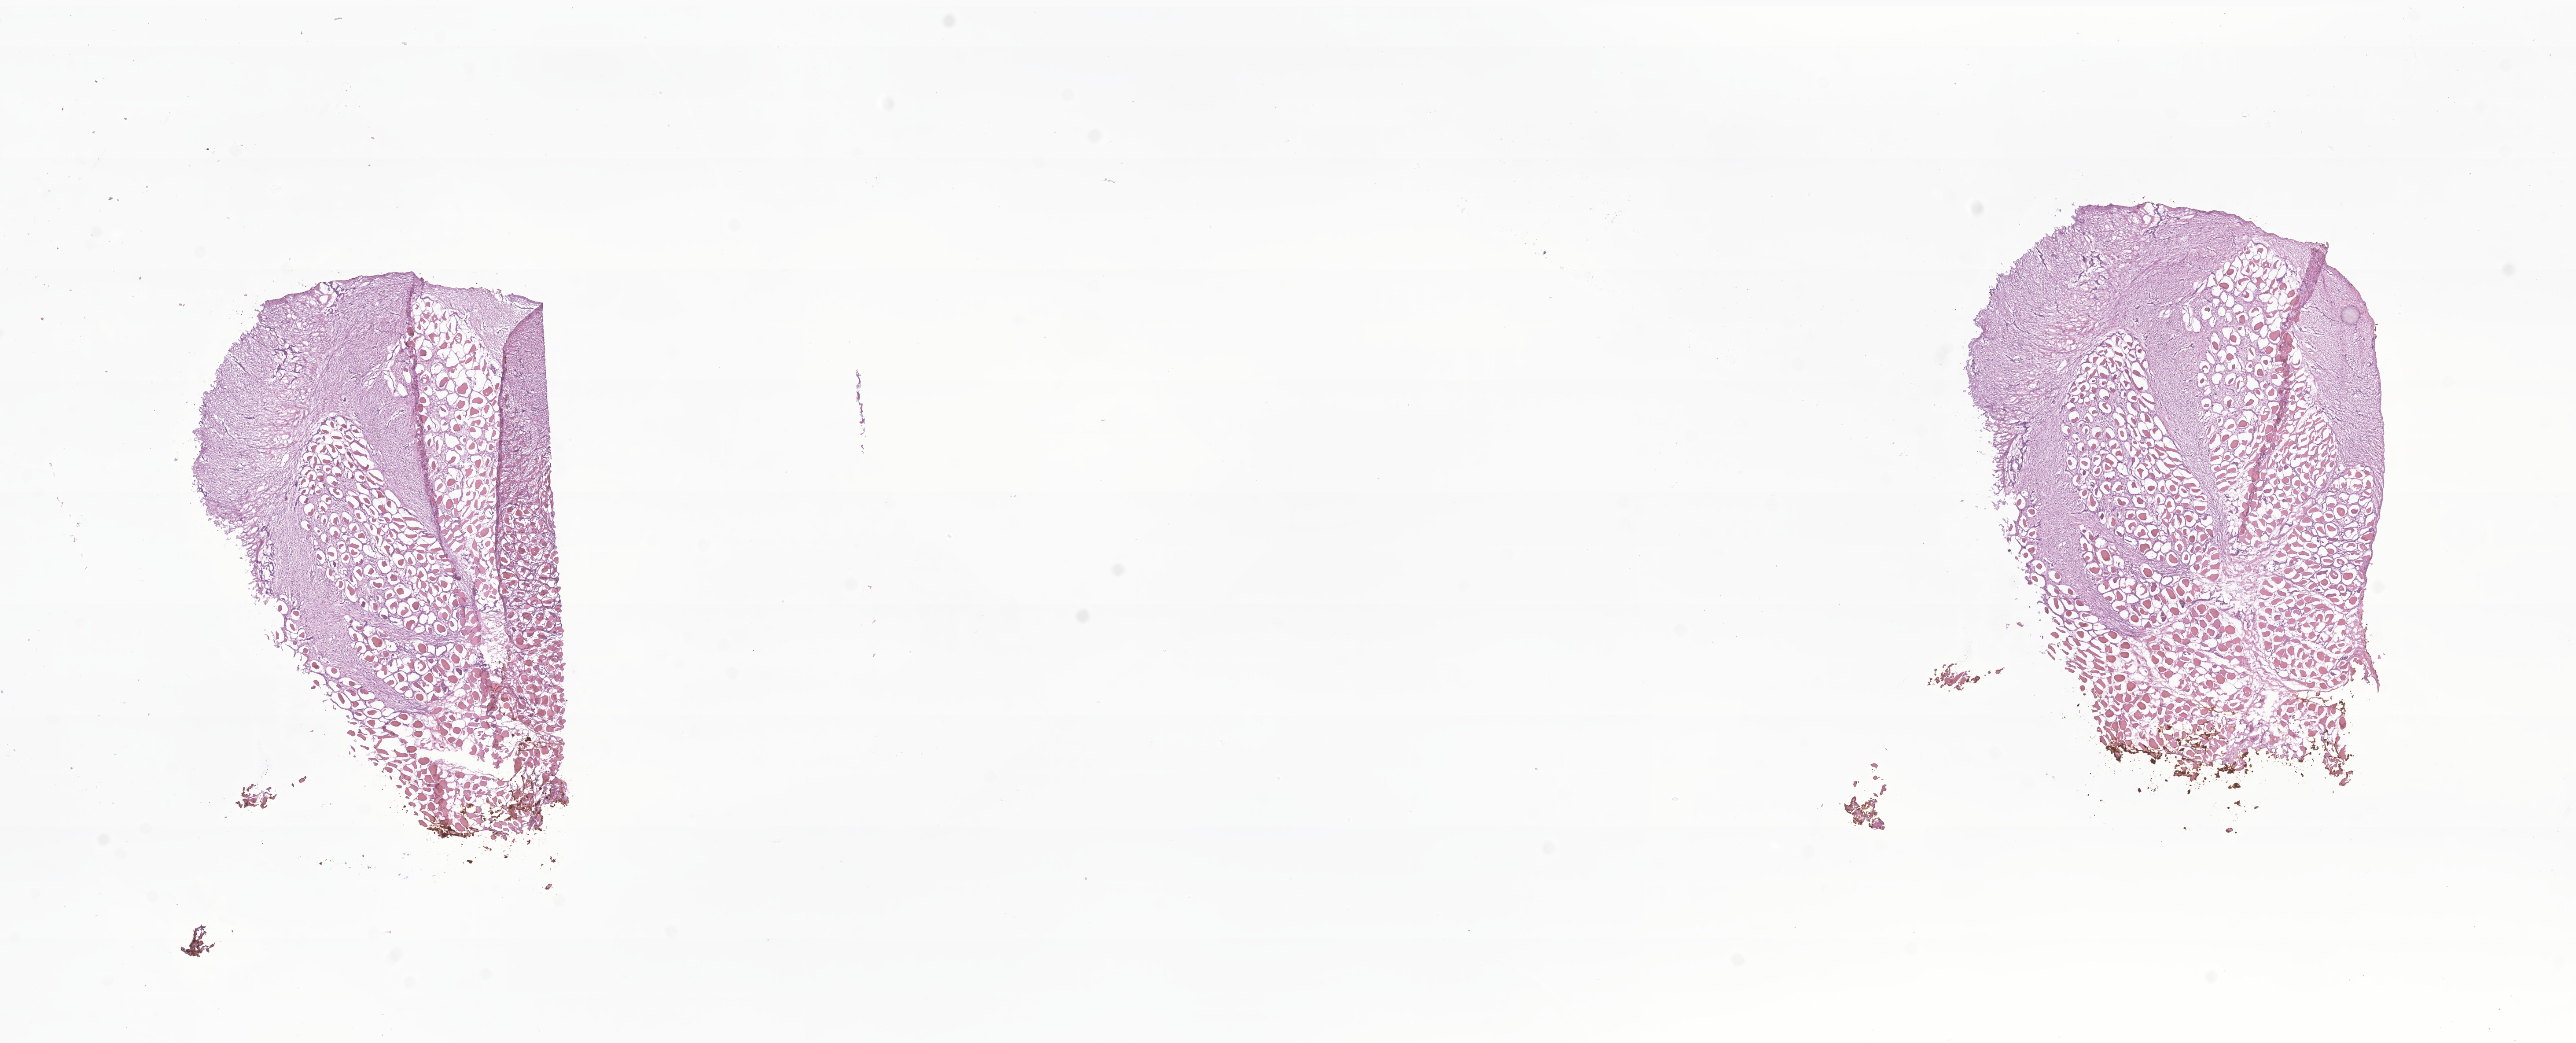
Whole-slide image, H&E stain of tumor tissue from the abdomen — whole scanned area (about 24.7 x 10.0 mm) shown as a low-resolution overview; frozen section. Female patient, age 212 months.
Diagnosis: Abdominal fibromatosis.